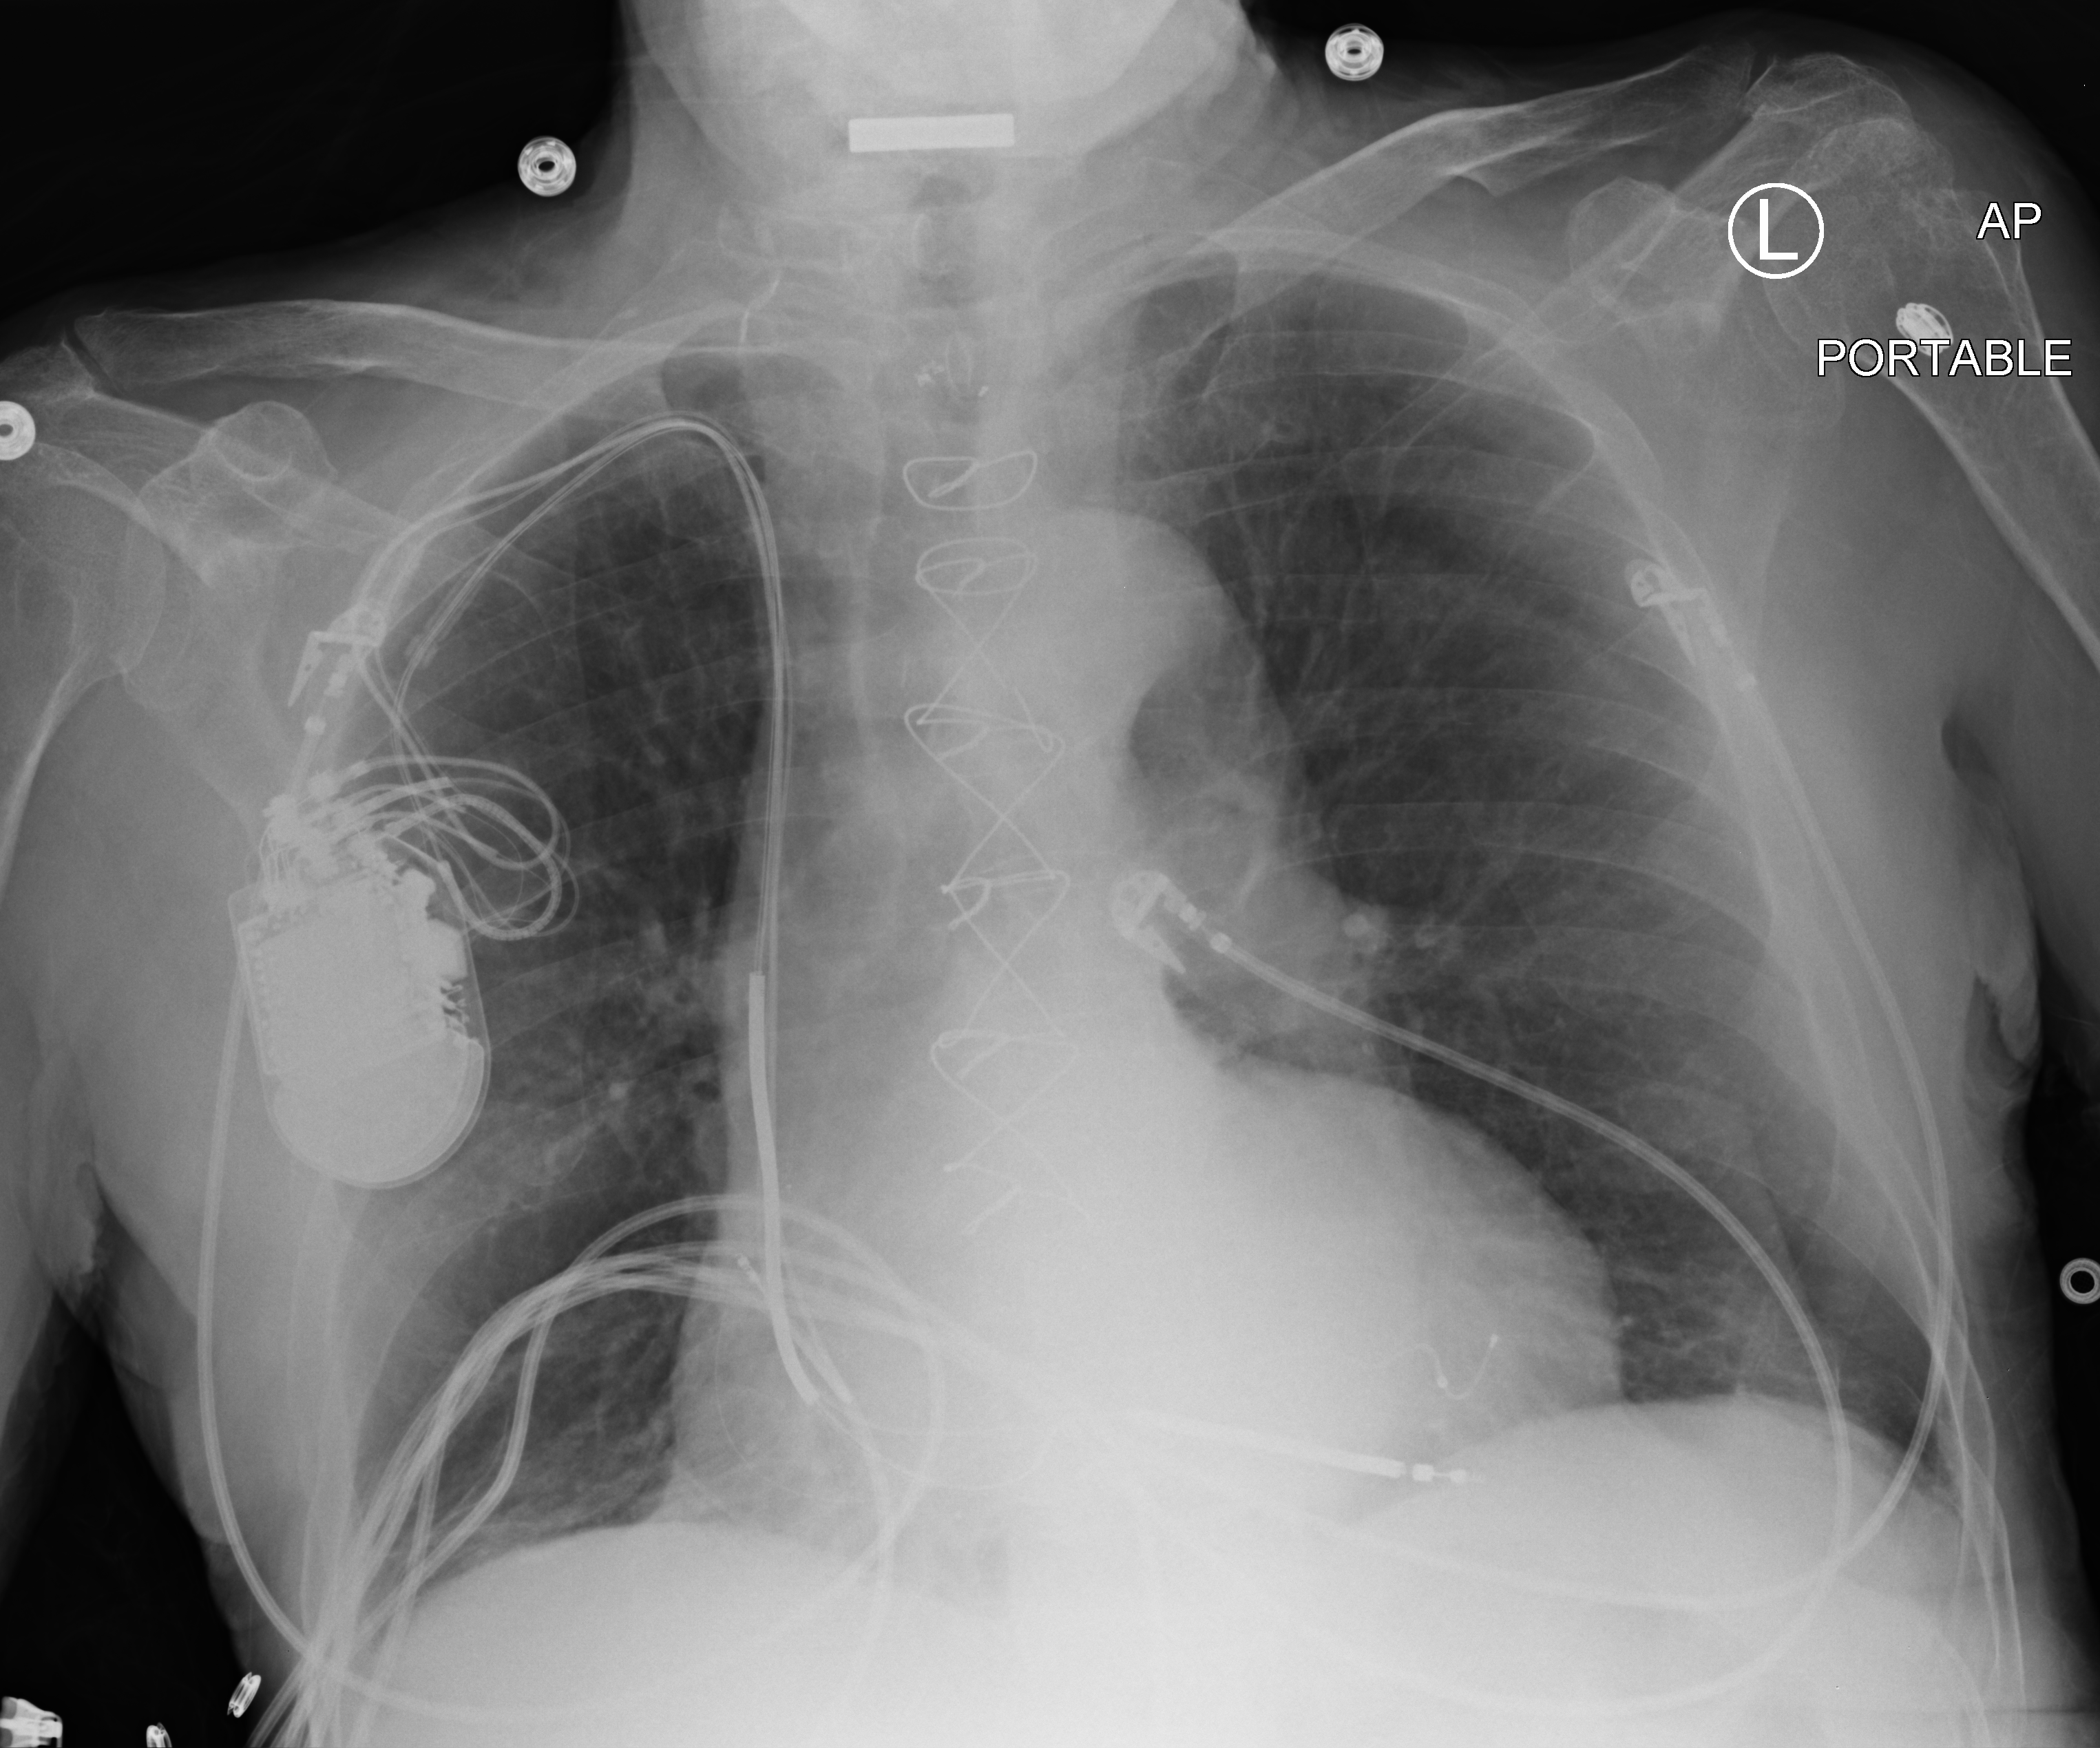
Bedside chest radiograph (computed radiography), anteroposterior (AP) projection. Male patient hospitalised with COVID-19, age 75–90 years.
Admission-level facts for this patient (not findings on this image; timing relative to this image not recorded):
- mechanically ventilated during this hospital stay: no
- length of hospital stay: 3 days